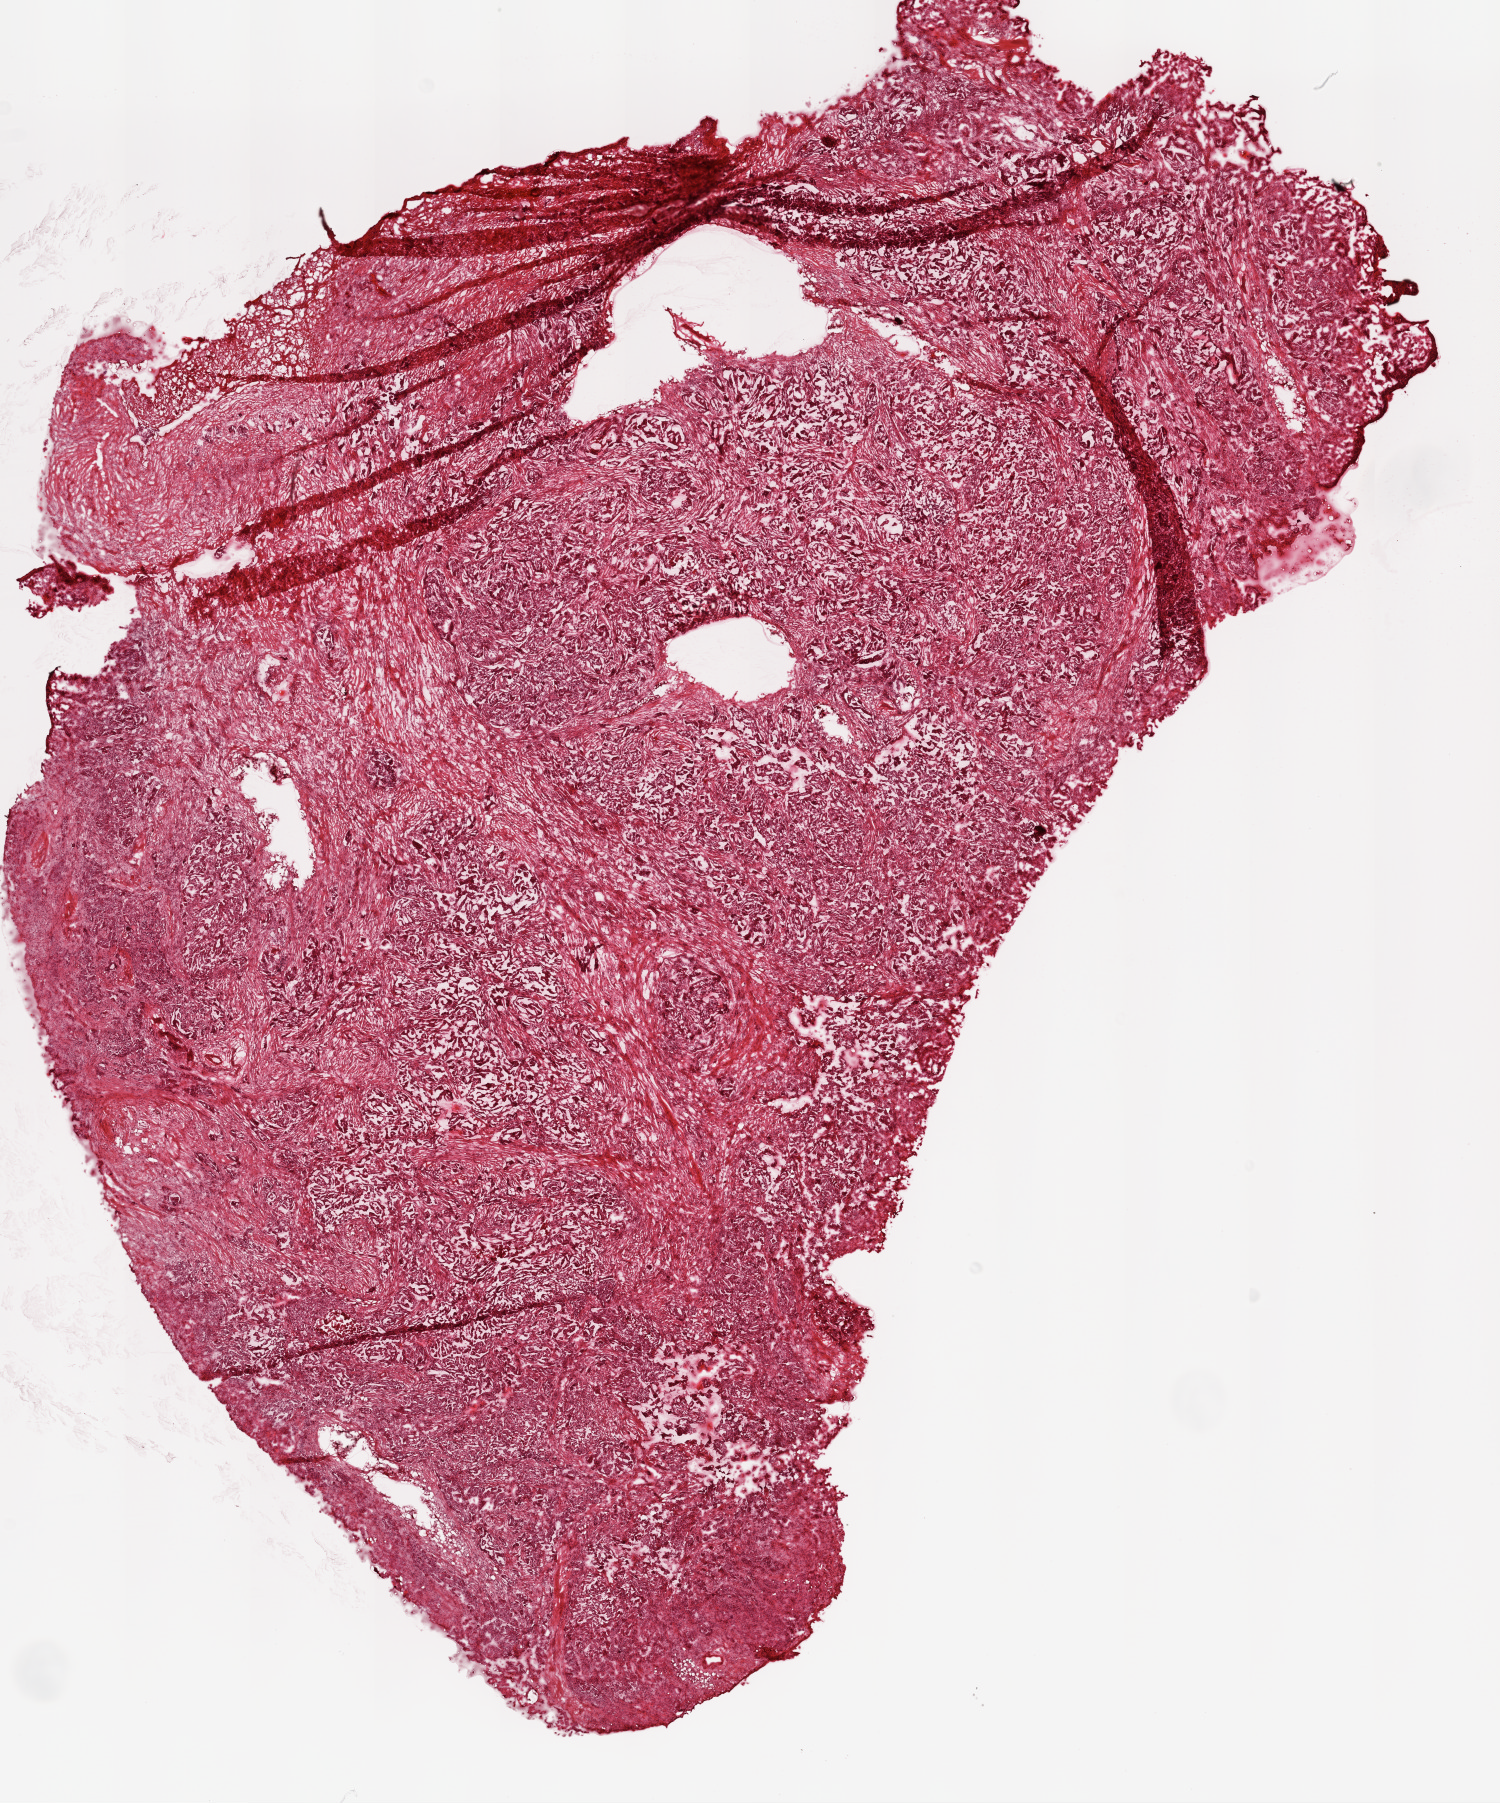
Digitized H&E tissue section (whole slide) — a low-resolution overview of the entire scanned area, about 12.0 x 14.5 mm. Frozen section from the top of the tissue portion. Primary tumour sample from the ovary. Patient: female, age at initial diagnosis 69 years. Histologic grade: G3 (poorly differentiated). Composition of this section per pathologist review: tumour cells 70%, tumour nuclei 80%, normal cells 0%, stromal cells 30%, necrosis 0%.
Pathologic diagnosis: Serous cystadenocarcinoma, NOS. Laterality: bilateral. FIGO stage: IIIC.